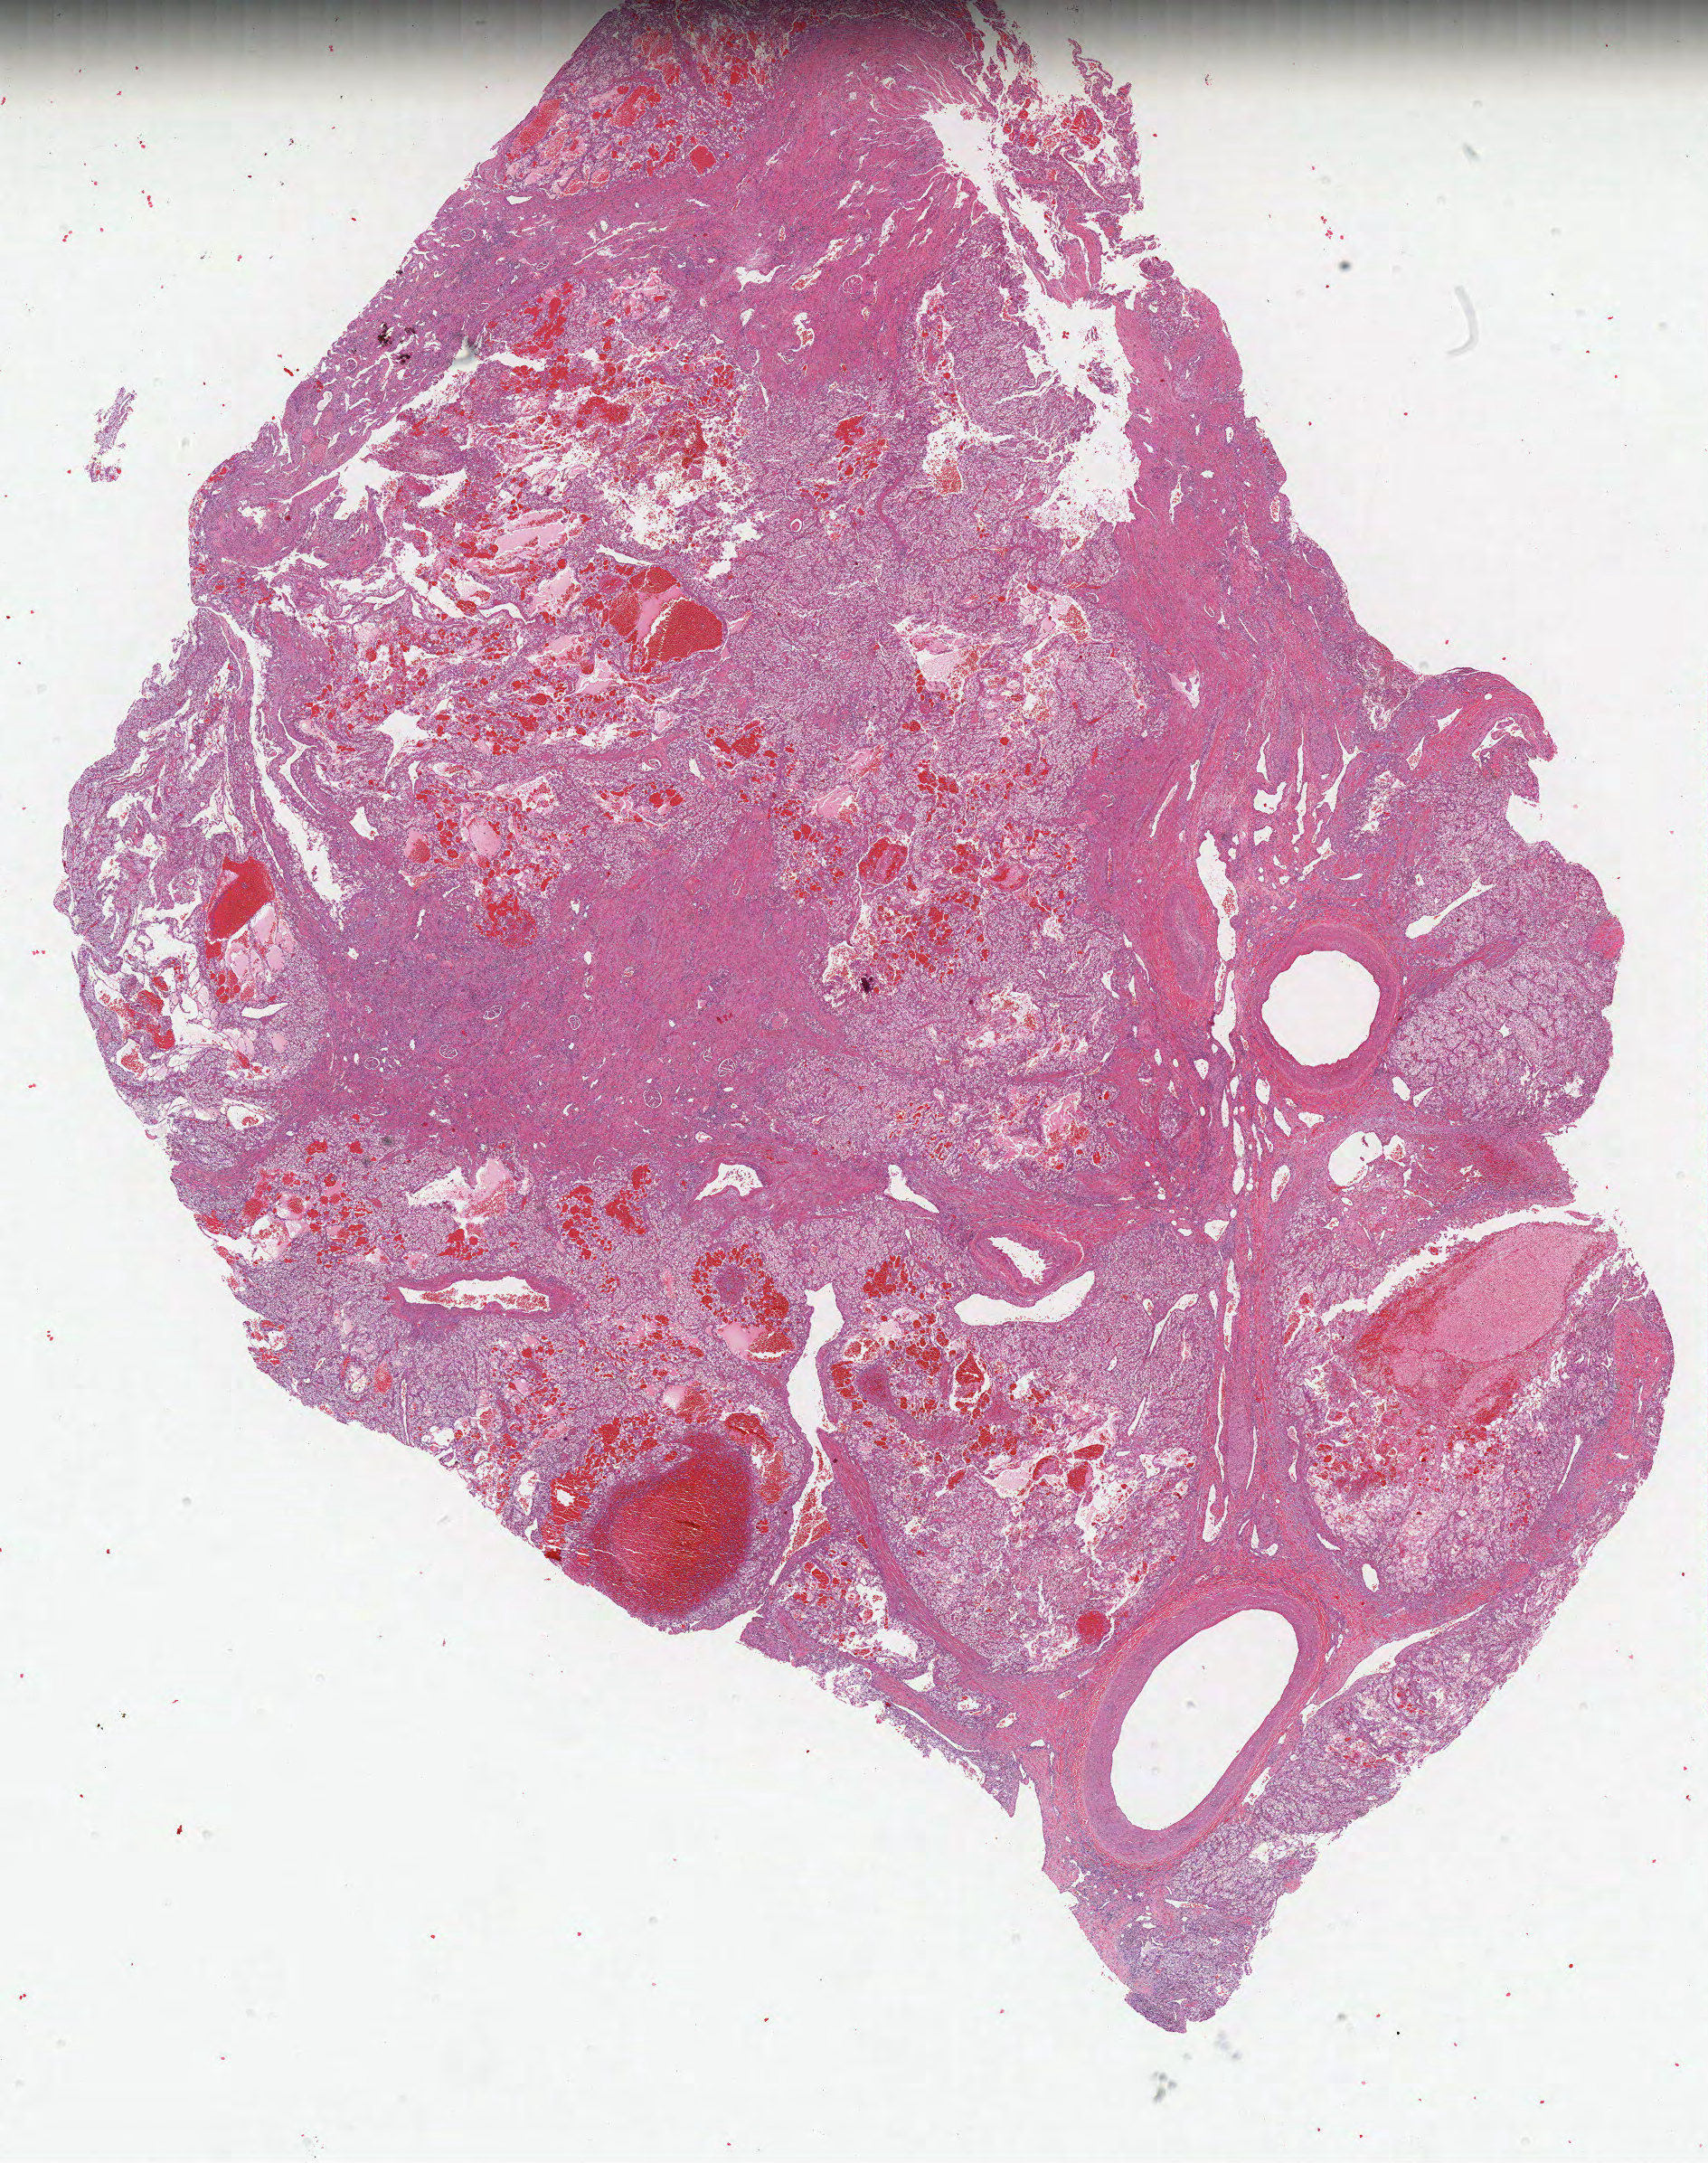
Hematoxylin and eosin (H&E) stained whole-slide image — low-resolution overview of the scanned area, about 15.1 x 19.1 mm, formalin-fixed paraffin-embedded (FFPE) diagnostic section, kidney, primary tumour sample. Patient: male, age at initial diagnosis 70 years. Histologic grade: G3 (poorly differentiated).
AJCC pathologic stage: III. Diagnosis: Clear cell adenocarcinoma, NOS.